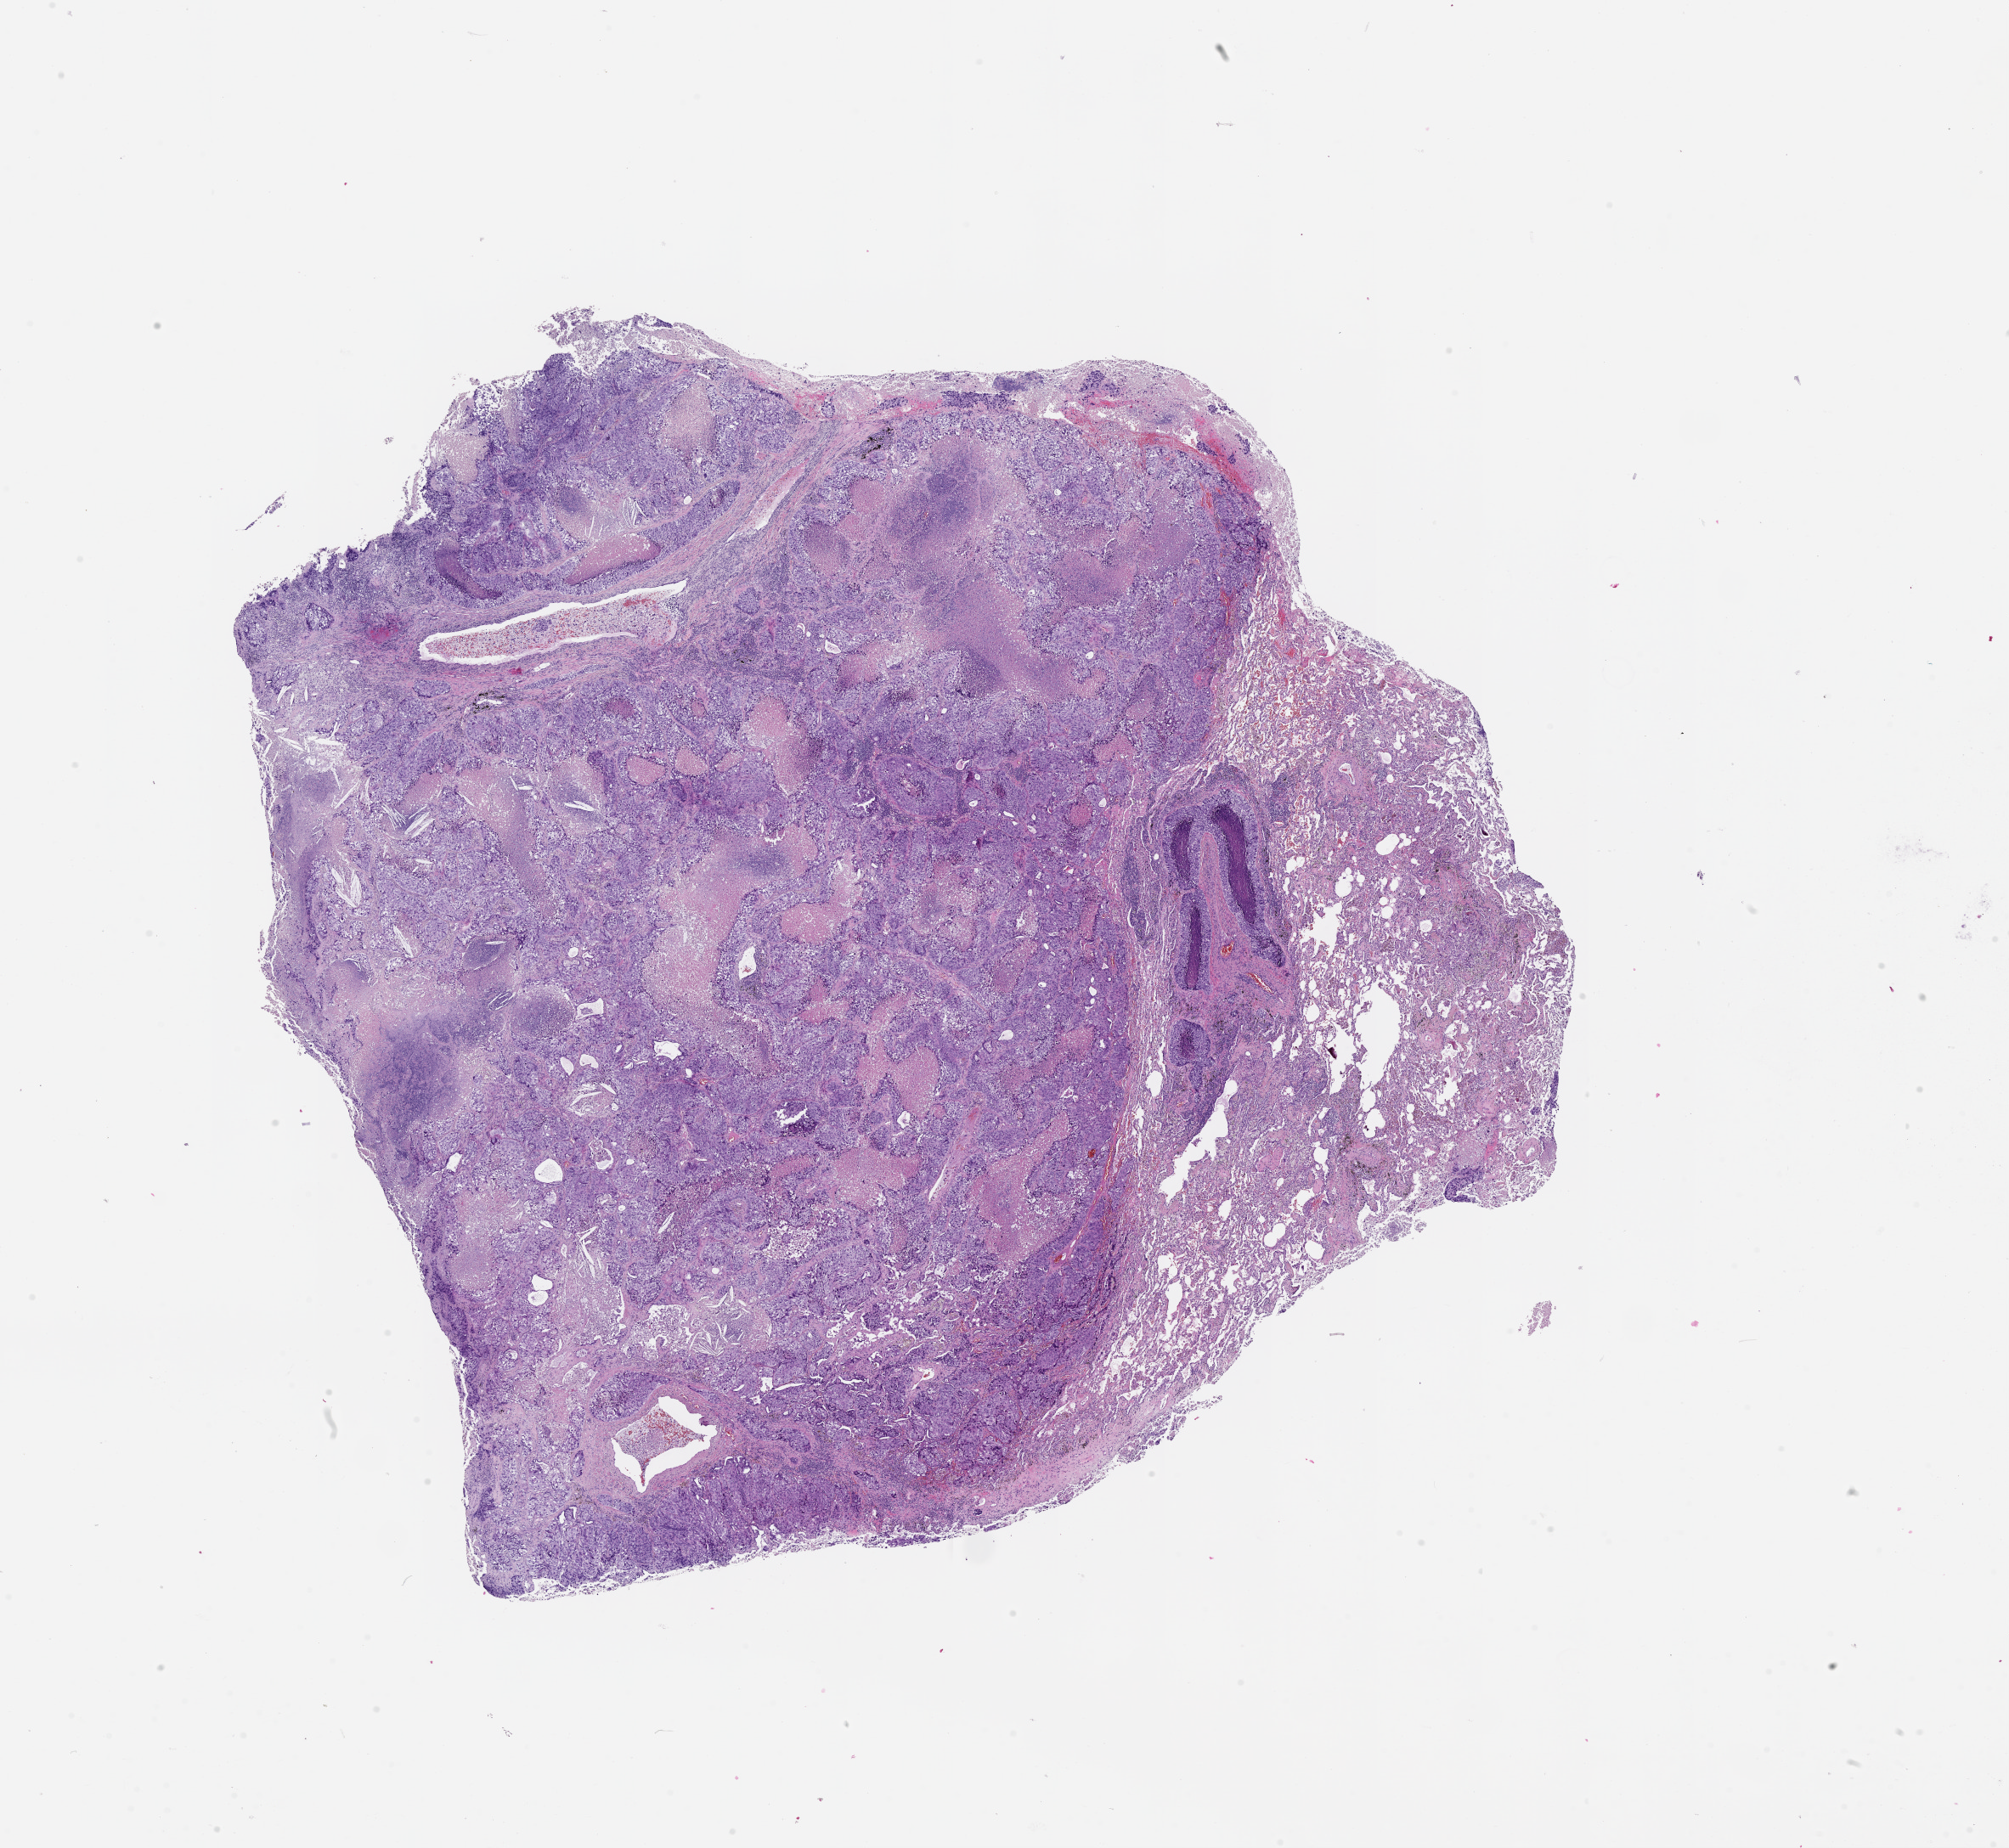
Digitized H&E tissue section (whole slide), shown as a low-resolution overview of the whole scanned area (about 19.0 x 17.5 mm, slide scanned at 20x). Lung, tumour tissue. Male, 54 y/o.
- patient diagnosis (cohort enrolment): squamous cell carcinoma (lung)